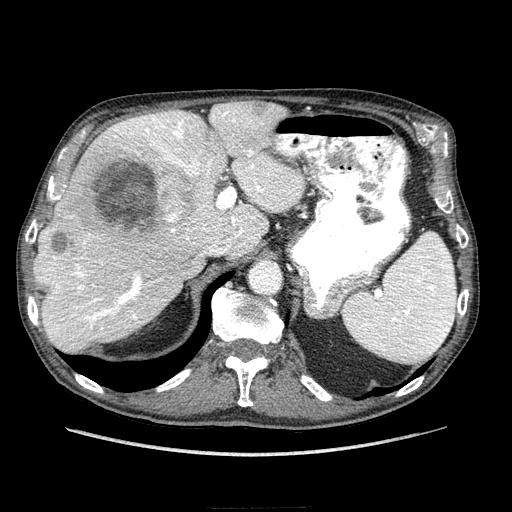
Contrast-enhanced abdominal CT (liver protocol), one axial slice. Slice 161 of 218 in the series (ordered by position). Reconstruction kernel STANDARD. Soft-tissue window (W 400 / L 40 HU). 512 × 512 image matrix. From the clinical record (not read from this slice): diagnosis: hepatocellular carcinoma (patient treated with transarterial chemoembolisation; whether this scan precedes or follows treatment is not stated here); TNM stage (as recorded): Stage-IIIA; Child-Pugh class: A; tumour differentiation: well differentiated; tumour nodularity: multinodular.
Annotated regions visible in this slice (semi-automatic segmentation, software-assisted and operator-edited):
- liver parenchyma outside the tumour (the mass and vessels are separate outlines, so this box may not span the whole liver): bounding box <34,102,302,352> (left, top, right, bottom; pixels)
- mass: <51,109,226,254>
- liver vessels: <39,109,299,334>